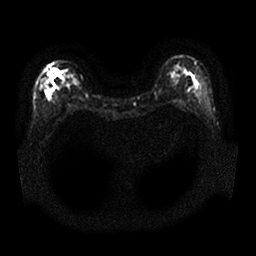
Breast MRI, one axial slice; position 12 of 25 along the scan axis; diffusion-weighted series; image 2 of 4 stored at this slice position (different b-values; order by instance number); 1.5 T; 4 mm slice thickness; 256 × 256 image matrix, field of view 340 × 340 mm. Female patient.
Structures marked on this image (manually delineated by an expert):
- tumour on diffusion-weighted imaging: bounding box (x1, y1, x2, y2) in pixels: (44, 65, 60, 81)